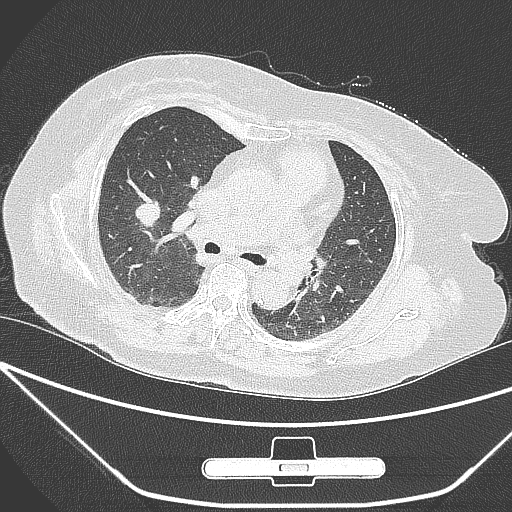
Chest CT, one axial slice; position 160 of 245 along the scan axis; 120 kVp; lung window (W 1500 / L -600 HU); 1 mm slice thickness; 512 × 512 image matrix. Patient: female, 65 years. From the clinical record (not read from this slice): clinical TNM (as recorded): T1c N0 M0.
Annotated regions visible in this slice (bounding box drawn by a radiologist):
- lung tumour (recorded histology: adenocarcinoma): bounding box <126,192,173,237> (left, top, right, bottom; pixels)